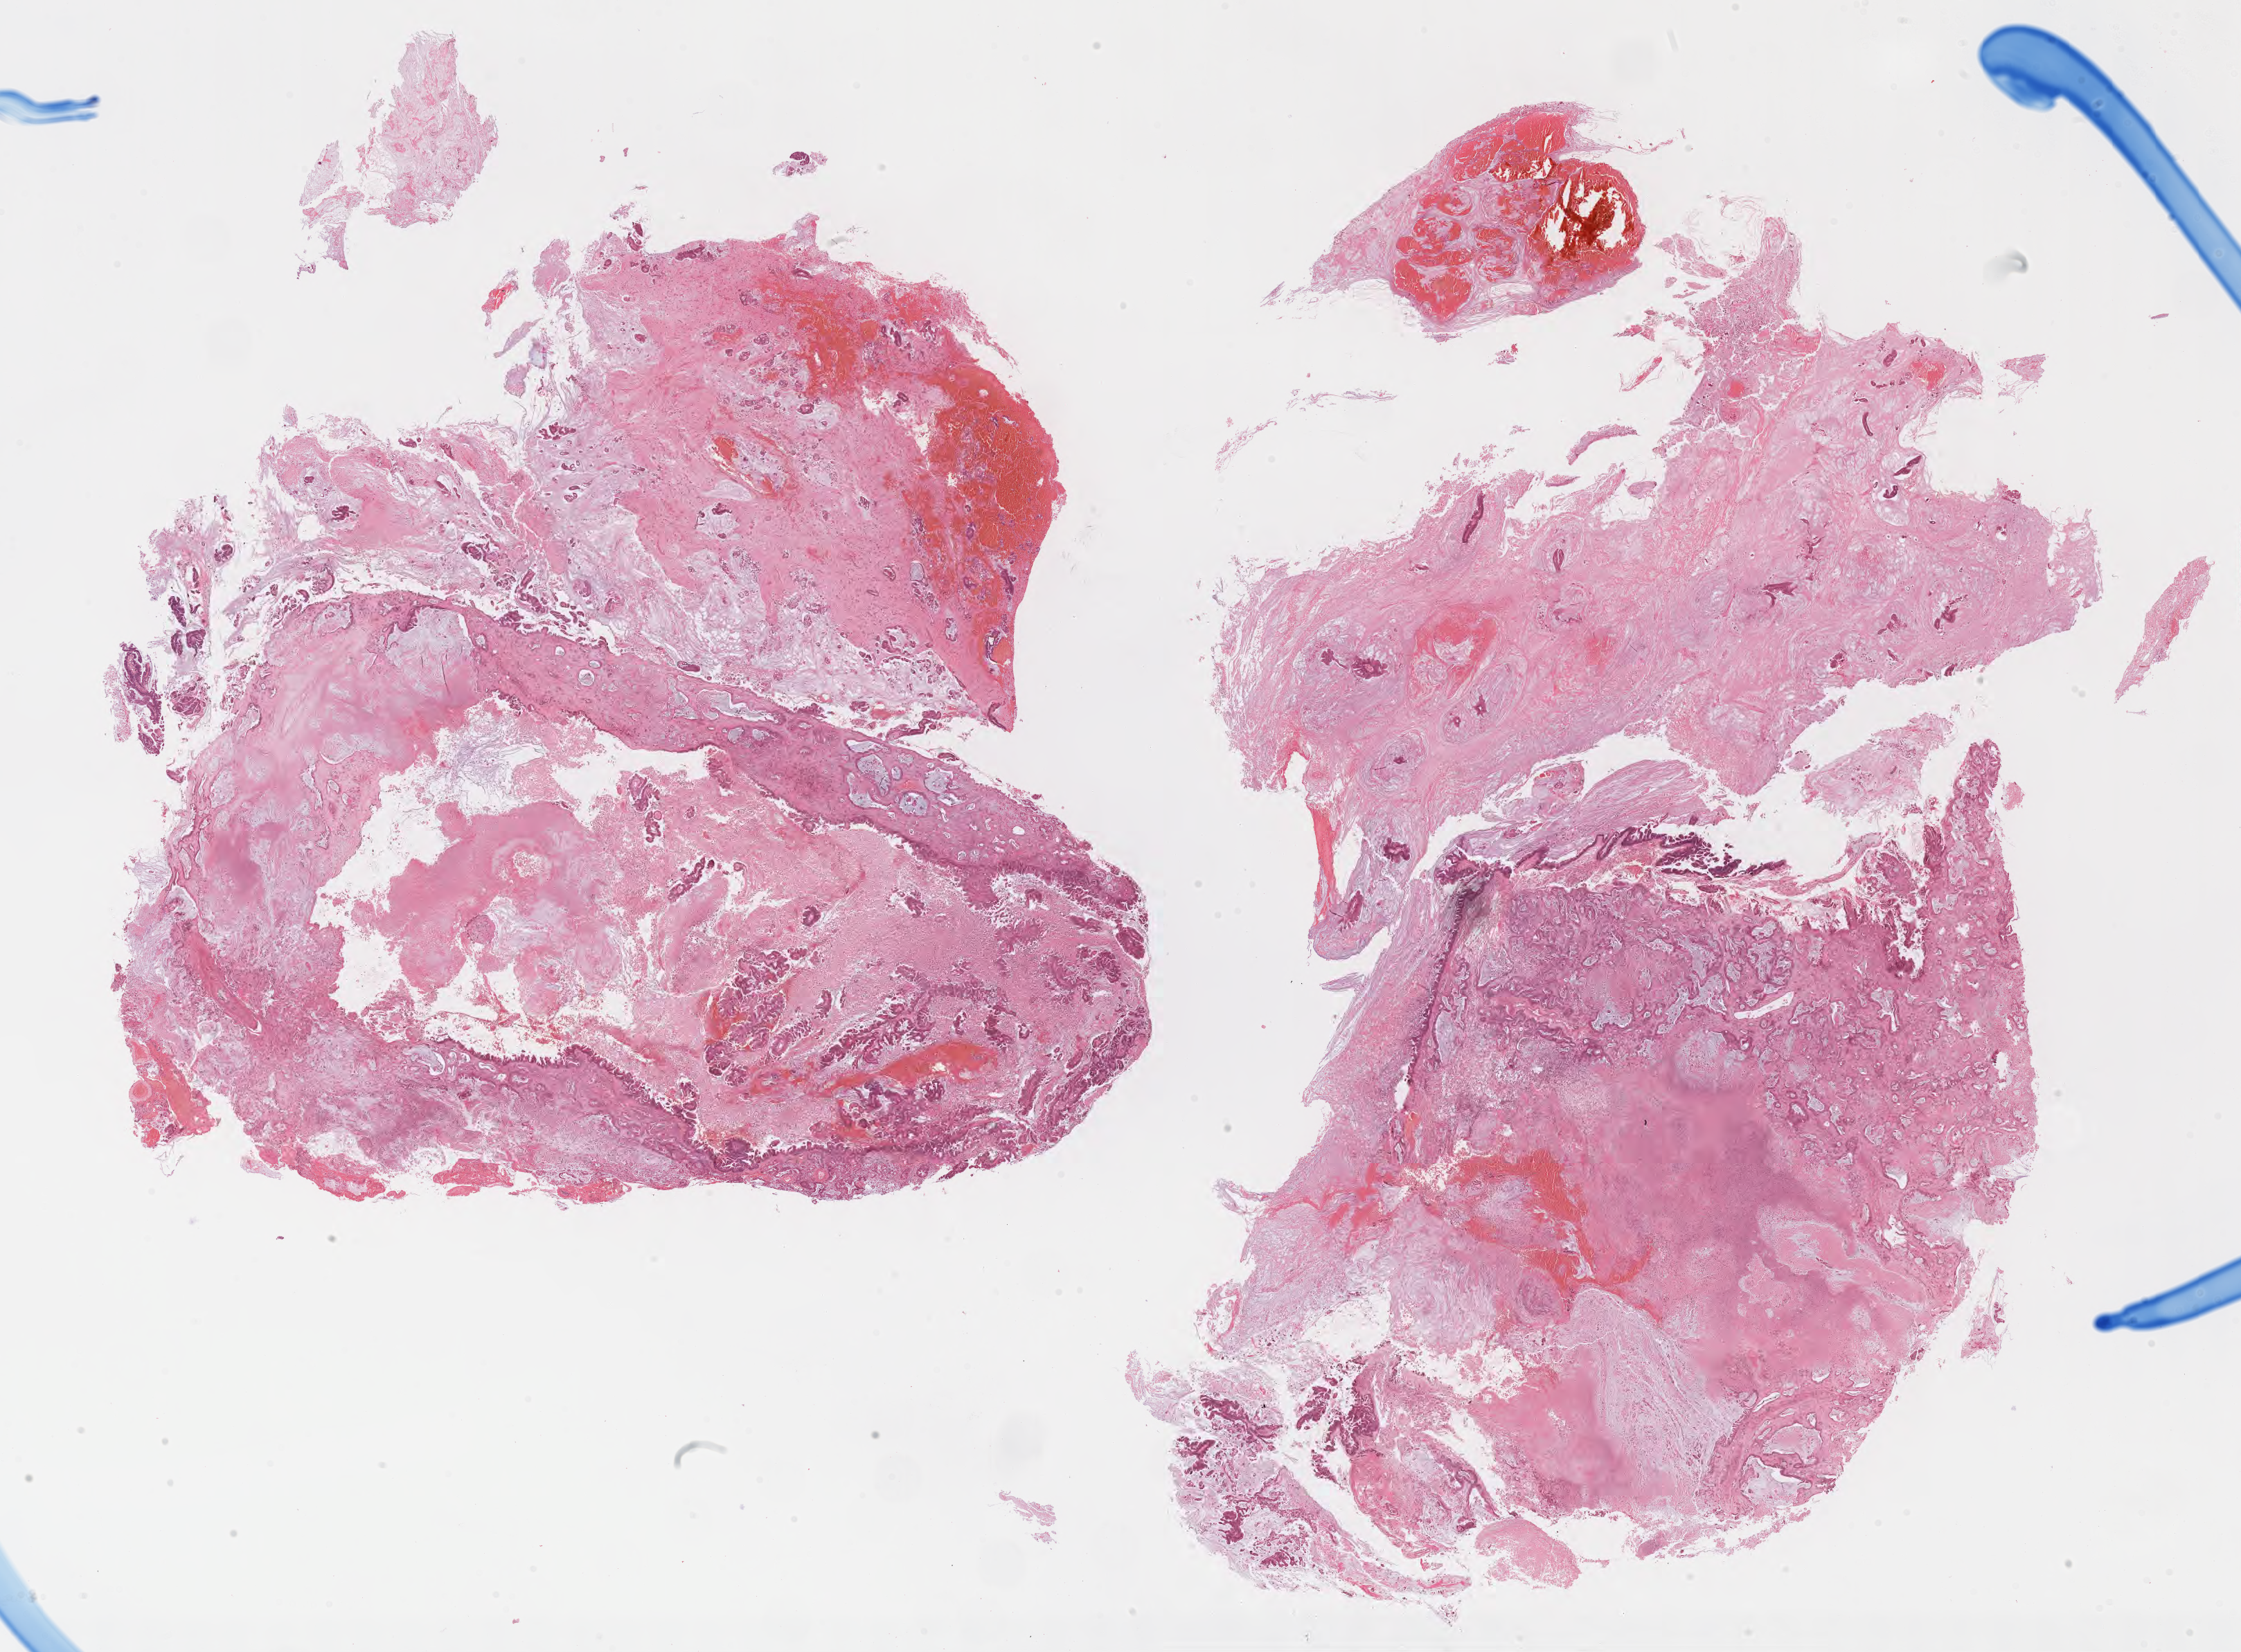
H&E whole-slide image — whole scanned area (about 26.2 x 19.3 mm) shown as a low-resolution overview. Formalin-fixed paraffin-embedded section. Metastatic tumor tissue, resected from brain. Male patient; age at initial diagnosis 68 years. Slide review estimates, as recorded: tumor cells 50%, tumor nuclei 50%, stromal cells 10%, necrosis 40%, normal cells 0%. Infiltration values recorded for this section: lymphocyte infiltration 2%, monocyte infiltration 1%, neutrophil infiltration 4%.
Patient diagnosis (primary): Small cell carcinoma, NOS.